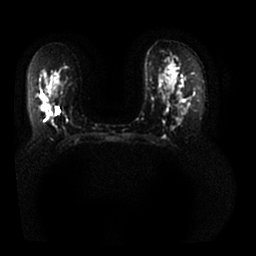
Breast MRI, one axial slice. Position 18 of 25 along the scan axis. Diffusion-weighted series; image 2 of 4 stored at this slice position (different b-values; order by instance number). 1.5 T. 4 mm slice thickness. 256 × 256 image matrix. Female patient.
Outlined on this slice (manually delineated by an expert):
- tumour on diffusion-weighted imaging: bounding box [x1, y1, x2, y2] px = [47, 110, 53, 117]